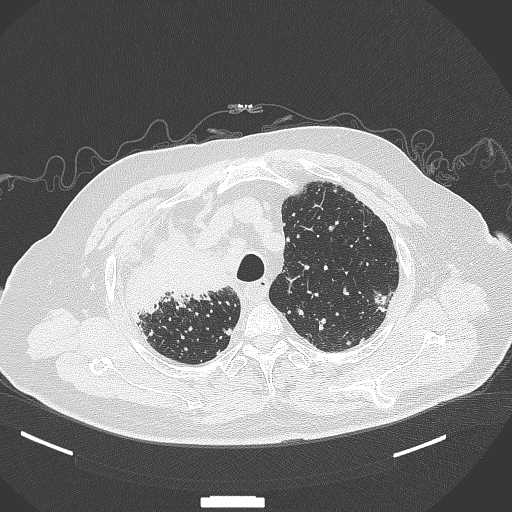
Chest CT, one axial slice; position 292 of 384 along the scan axis; reconstruction kernel B70f; lung window (W 1500 / L -600 HU); 1 mm slice thickness; 512 × 512 image matrix. Male patient, age 69 years. From the clinical record (not read from this slice): clinical TNM (as recorded): T4 N3 M1.
Outlined on this slice (rectangle marked by the reading radiologist):
- lung tumour (recorded histology: adenocarcinoma): bounding box <126,211,232,316> (left, top, right, bottom; pixels)